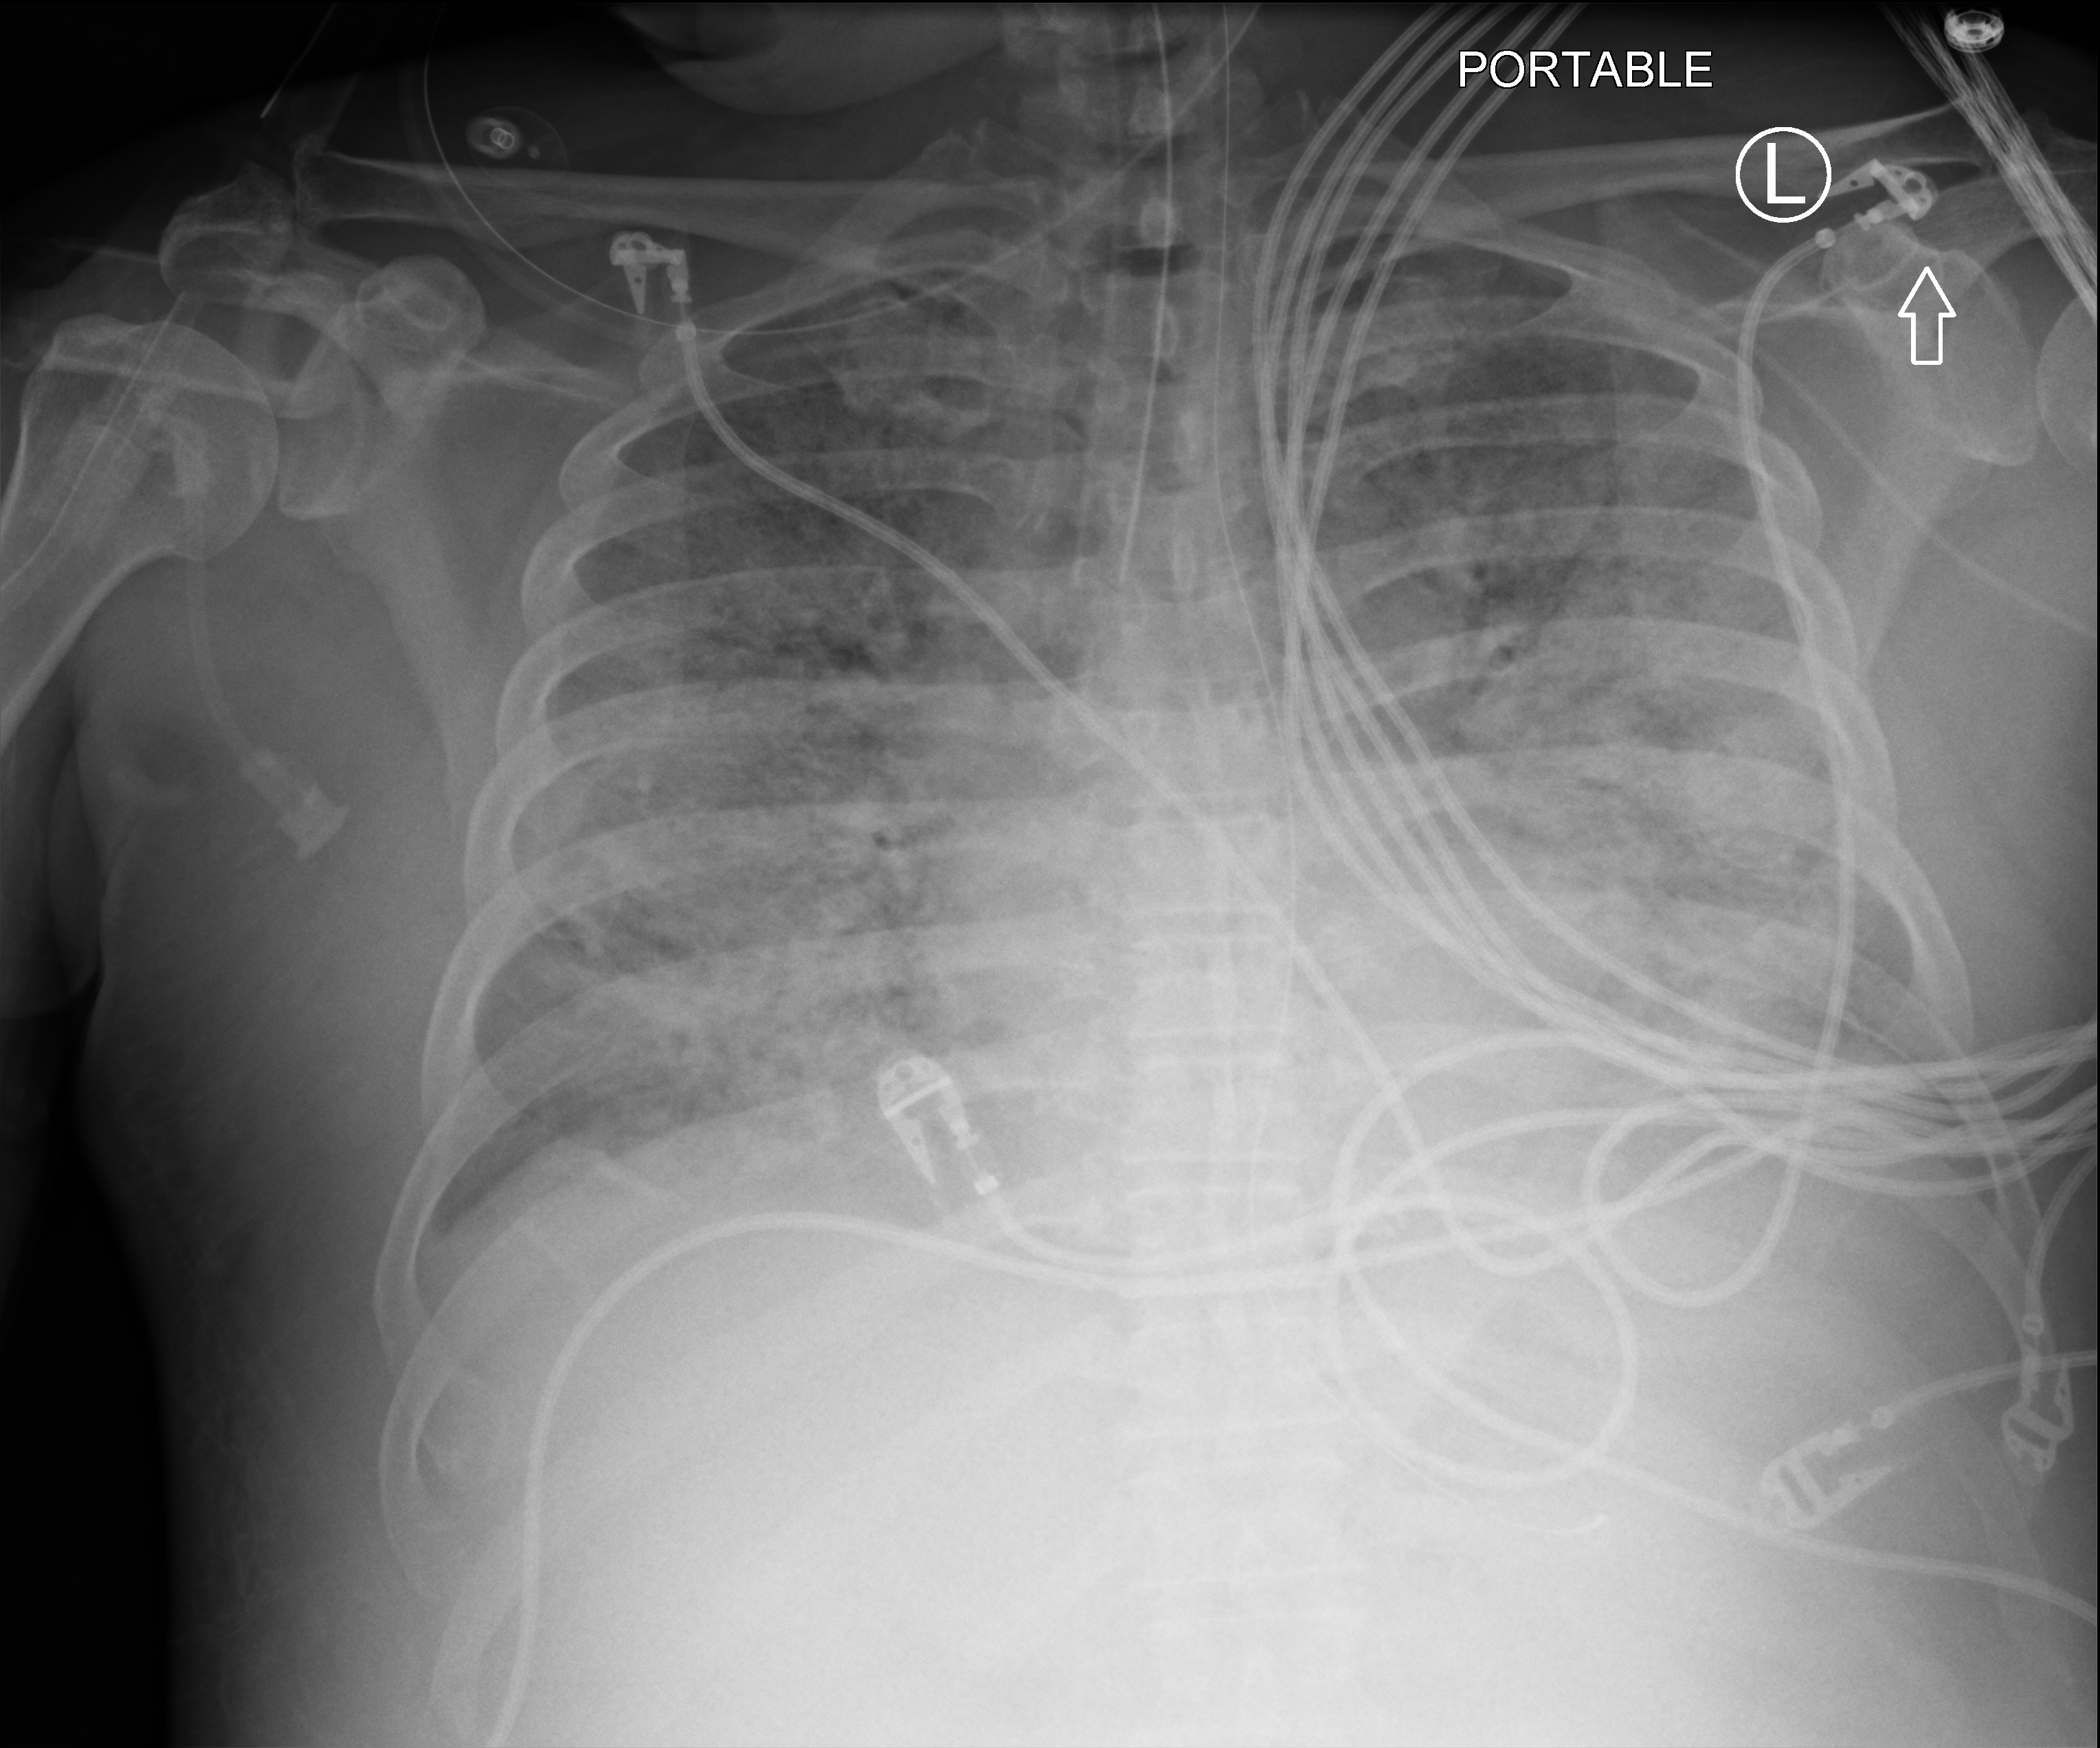
Portable chest radiograph. Patient hospitalised with COVID-19; male, aged 60–74 years.
From the hospital-stay record, not from the radiograph (when in the stay this image was taken is not recorded): hypertension (admission record): yes; mechanically ventilated during this hospital stay: yes; admitted to intensive care during this hospital stay: yes.